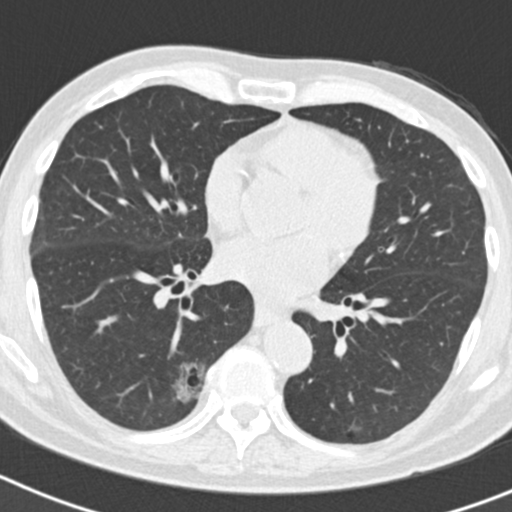
Axial slice from a low-dose chest CT screening exam, second annual screen, lung window (W 1500 / L -600 HU), 2 mm slice thickness, 120 kVp, slice 94 of 186 in the series, 512 × 512 image matrix, field of view 300 × 300 mm. Male, age 70 years at enrolment. Current smoker at enrolment.
• Expert reader's lesion annotation, box from (x=125, y=360) to (x=207, y=430) px.
• The screening reader recorded 5 non-calcified nodules or masses ≥4 mm on this exam; which of them this box marks is not recorded.
• Official screen result: positive, other.